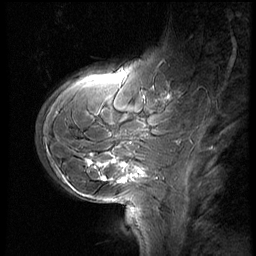
Breast MRI (dynamic contrast-enhanced), one sagittal slice; position 17 of 60 along the scan axis; 3 images stored at this slice position (order not interpretable as contrast timing); 1.5 T; TE 4.2 ms, TR 8.9 ms; 2.5 mm slice thickness; 256 × 256 image matrix. Patient: female, 29 years. From the clinical record (not read from this slice): setting: breast cancer imaged before/during neoadjuvant chemotherapy.
Structures marked on this image (semi-automatic segmentation, software-assisted and operator-edited):
- analysis volume of interest (the breast-tissue region the enhancement analysis was run in; not a lesion): bounding box [x1, y1, x2, y2] px = [37, 57, 185, 200]
- tumour enhancement mask (voxels above the 140 % enhancement threshold inside the analysis volume of interest): [88, 87, 155, 183]